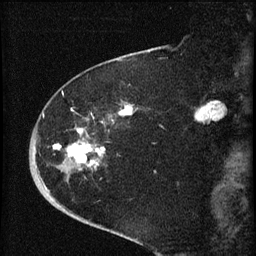
Breast MRI (dynamic contrast-enhanced), one sagittal slice. Position 20 of 60 along the scan axis. Dynamic contrast-enhanced series, image 2 of 4 at this slice position (ordered by acquisition). 1.5 T. TE 4.2 ms, TR 8.2 ms. 2 mm slice thickness. 256 × 256 image matrix, field of view 180 × 180 mm. Patient: female, 71 years.
Outlined on this slice (semi-automatically segmented with operator editing):
- analysis volume of interest (the breast-tissue region the enhancement analysis was run in; not a lesion): bounding box <35,75,136,190> (left, top, right, bottom; pixels)
- tumour enhancement mask (voxels above the 70 % enhancement threshold inside the analysis volume of interest): <45,106,133,188>